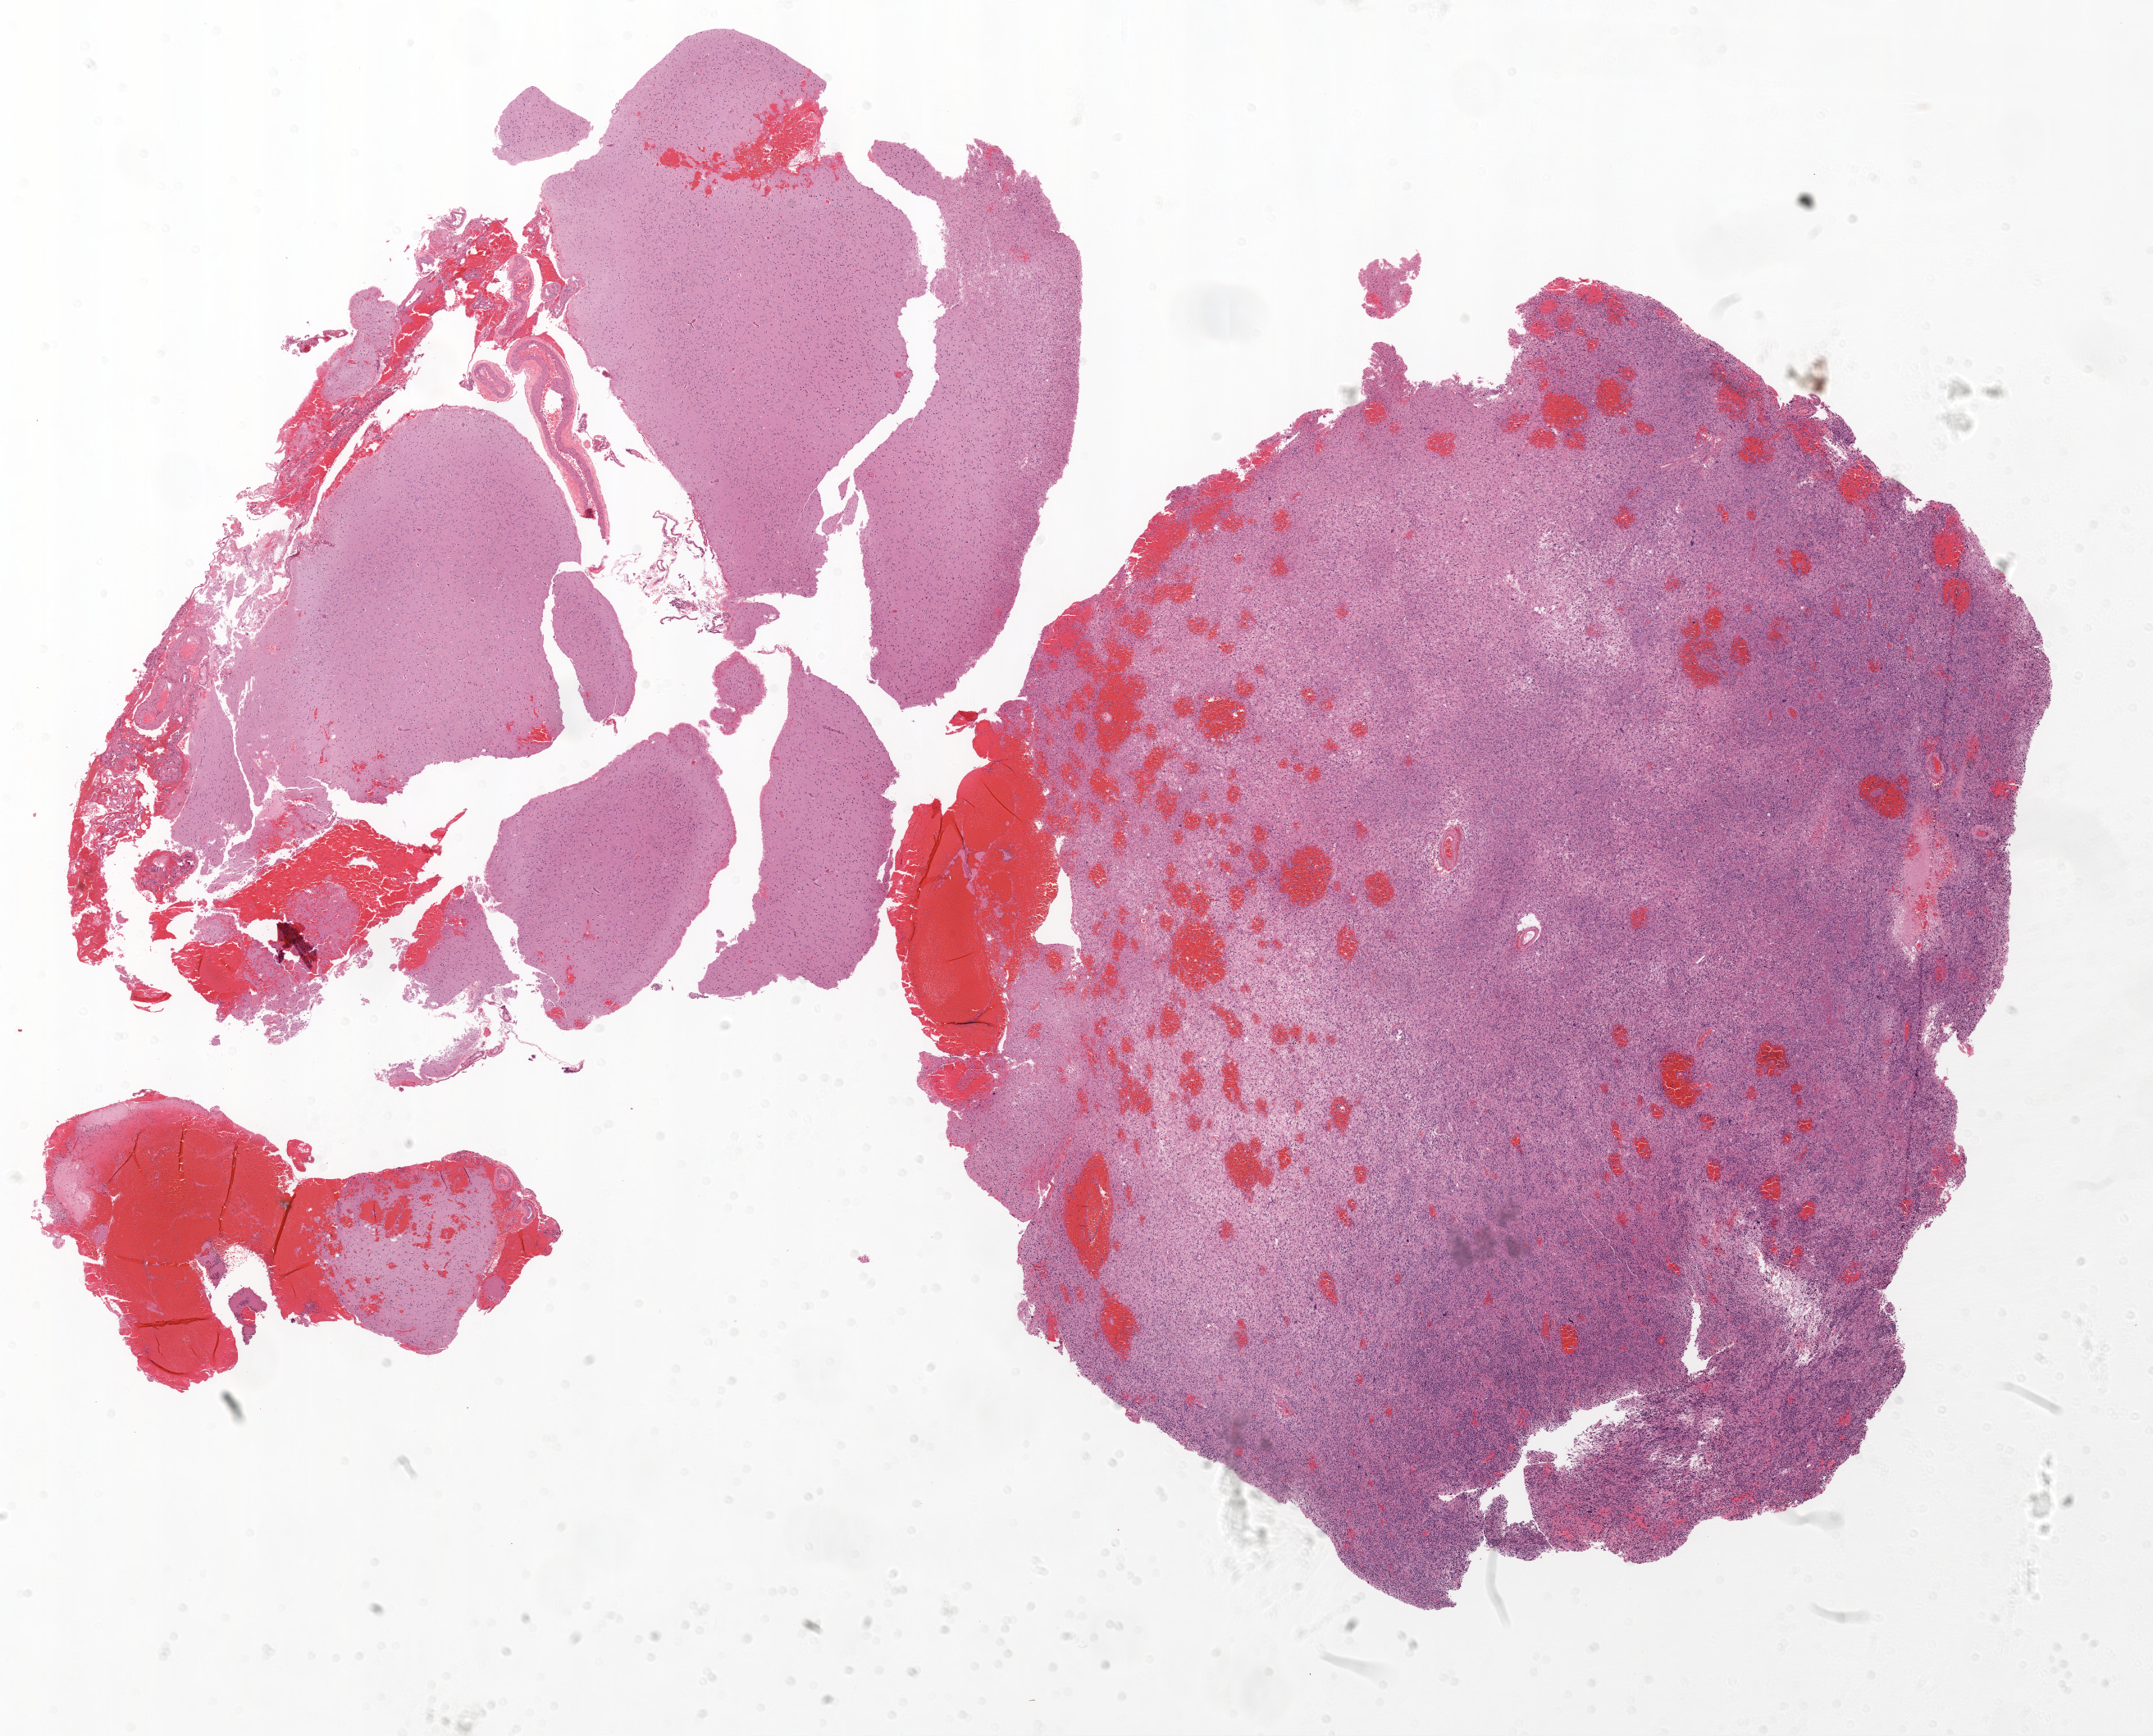
Digitized H&E-stained tissue section (whole slide), whole scanned area (about 21.1 x 17.0 mm, from a 20x scan) shown as a low-resolution overview; formalin-fixed paraffin-embedded (FFPE) diagnostic section; brain, primary tumour sample. Patient: male, age at initial diagnosis 65 years.
Diagnosis: Glioblastoma.